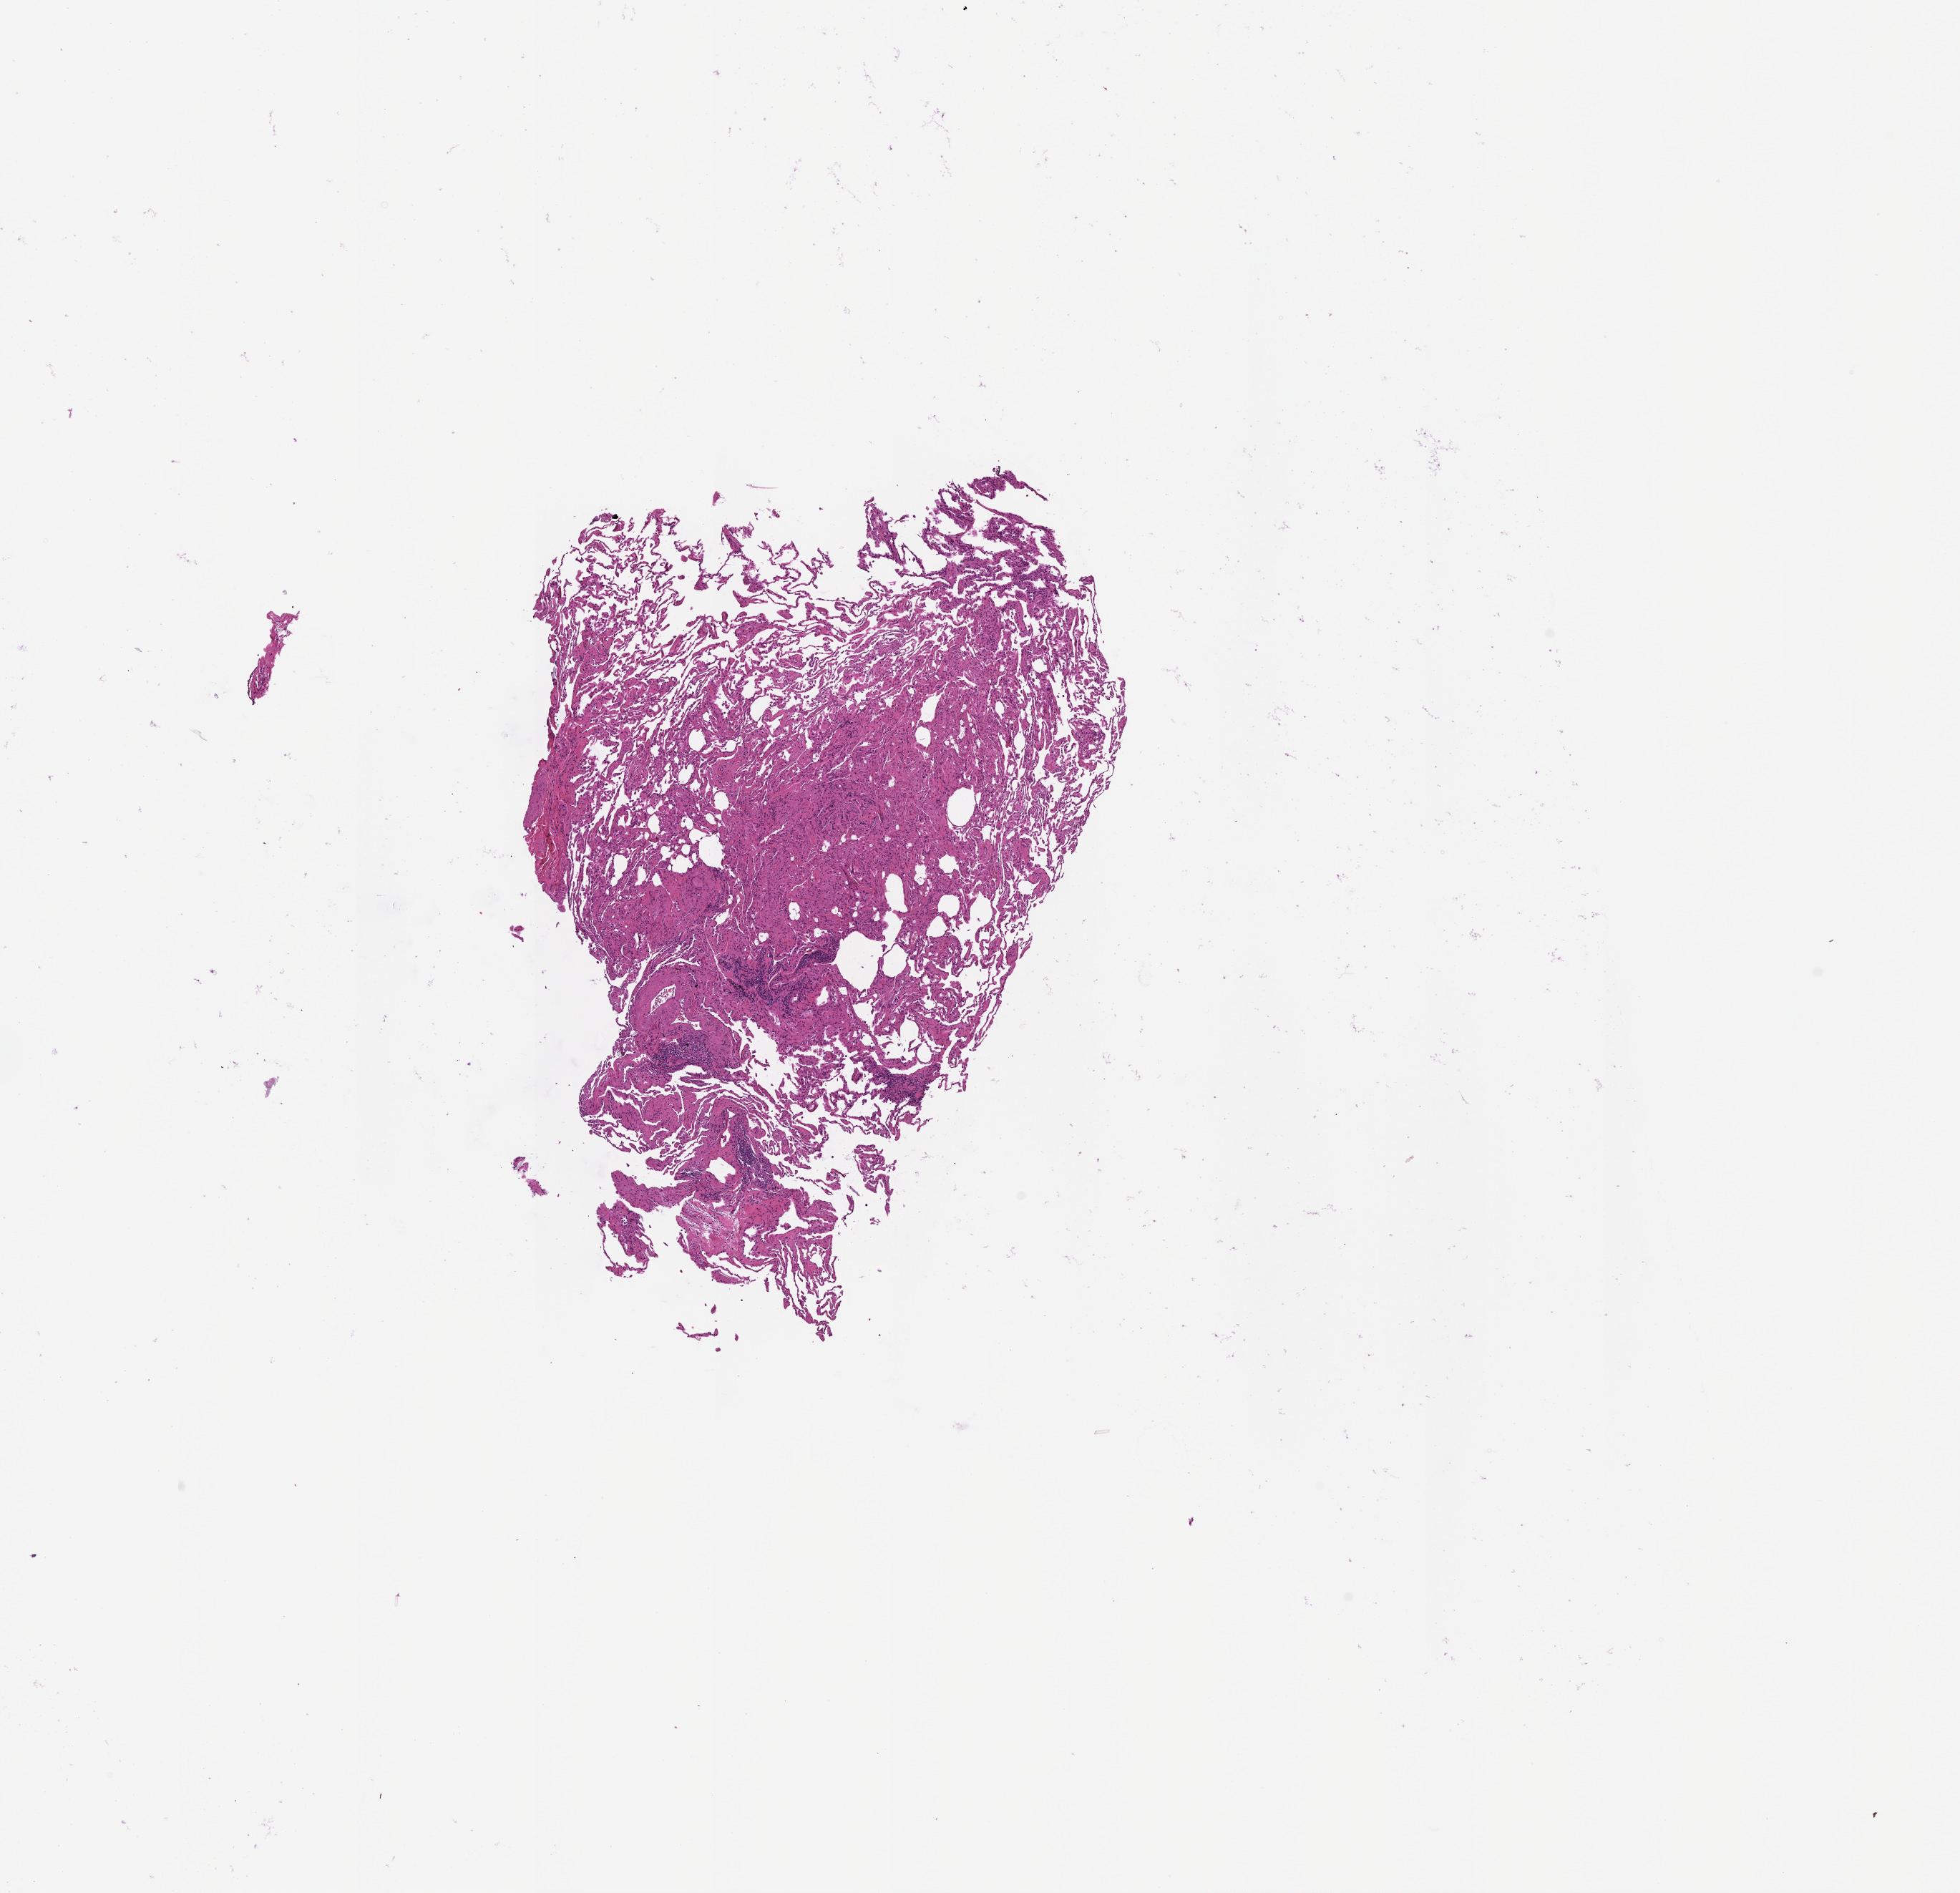
Whole-slide histology image, H&E-stained, whole scanned area (about 11.0 x 10.6 mm, slide scanned at 20x) shown as a low-resolution overview. Lung, tissue type not recorded.
* patient diagnosis (cohort enrolment): squamous cell carcinoma (lung)